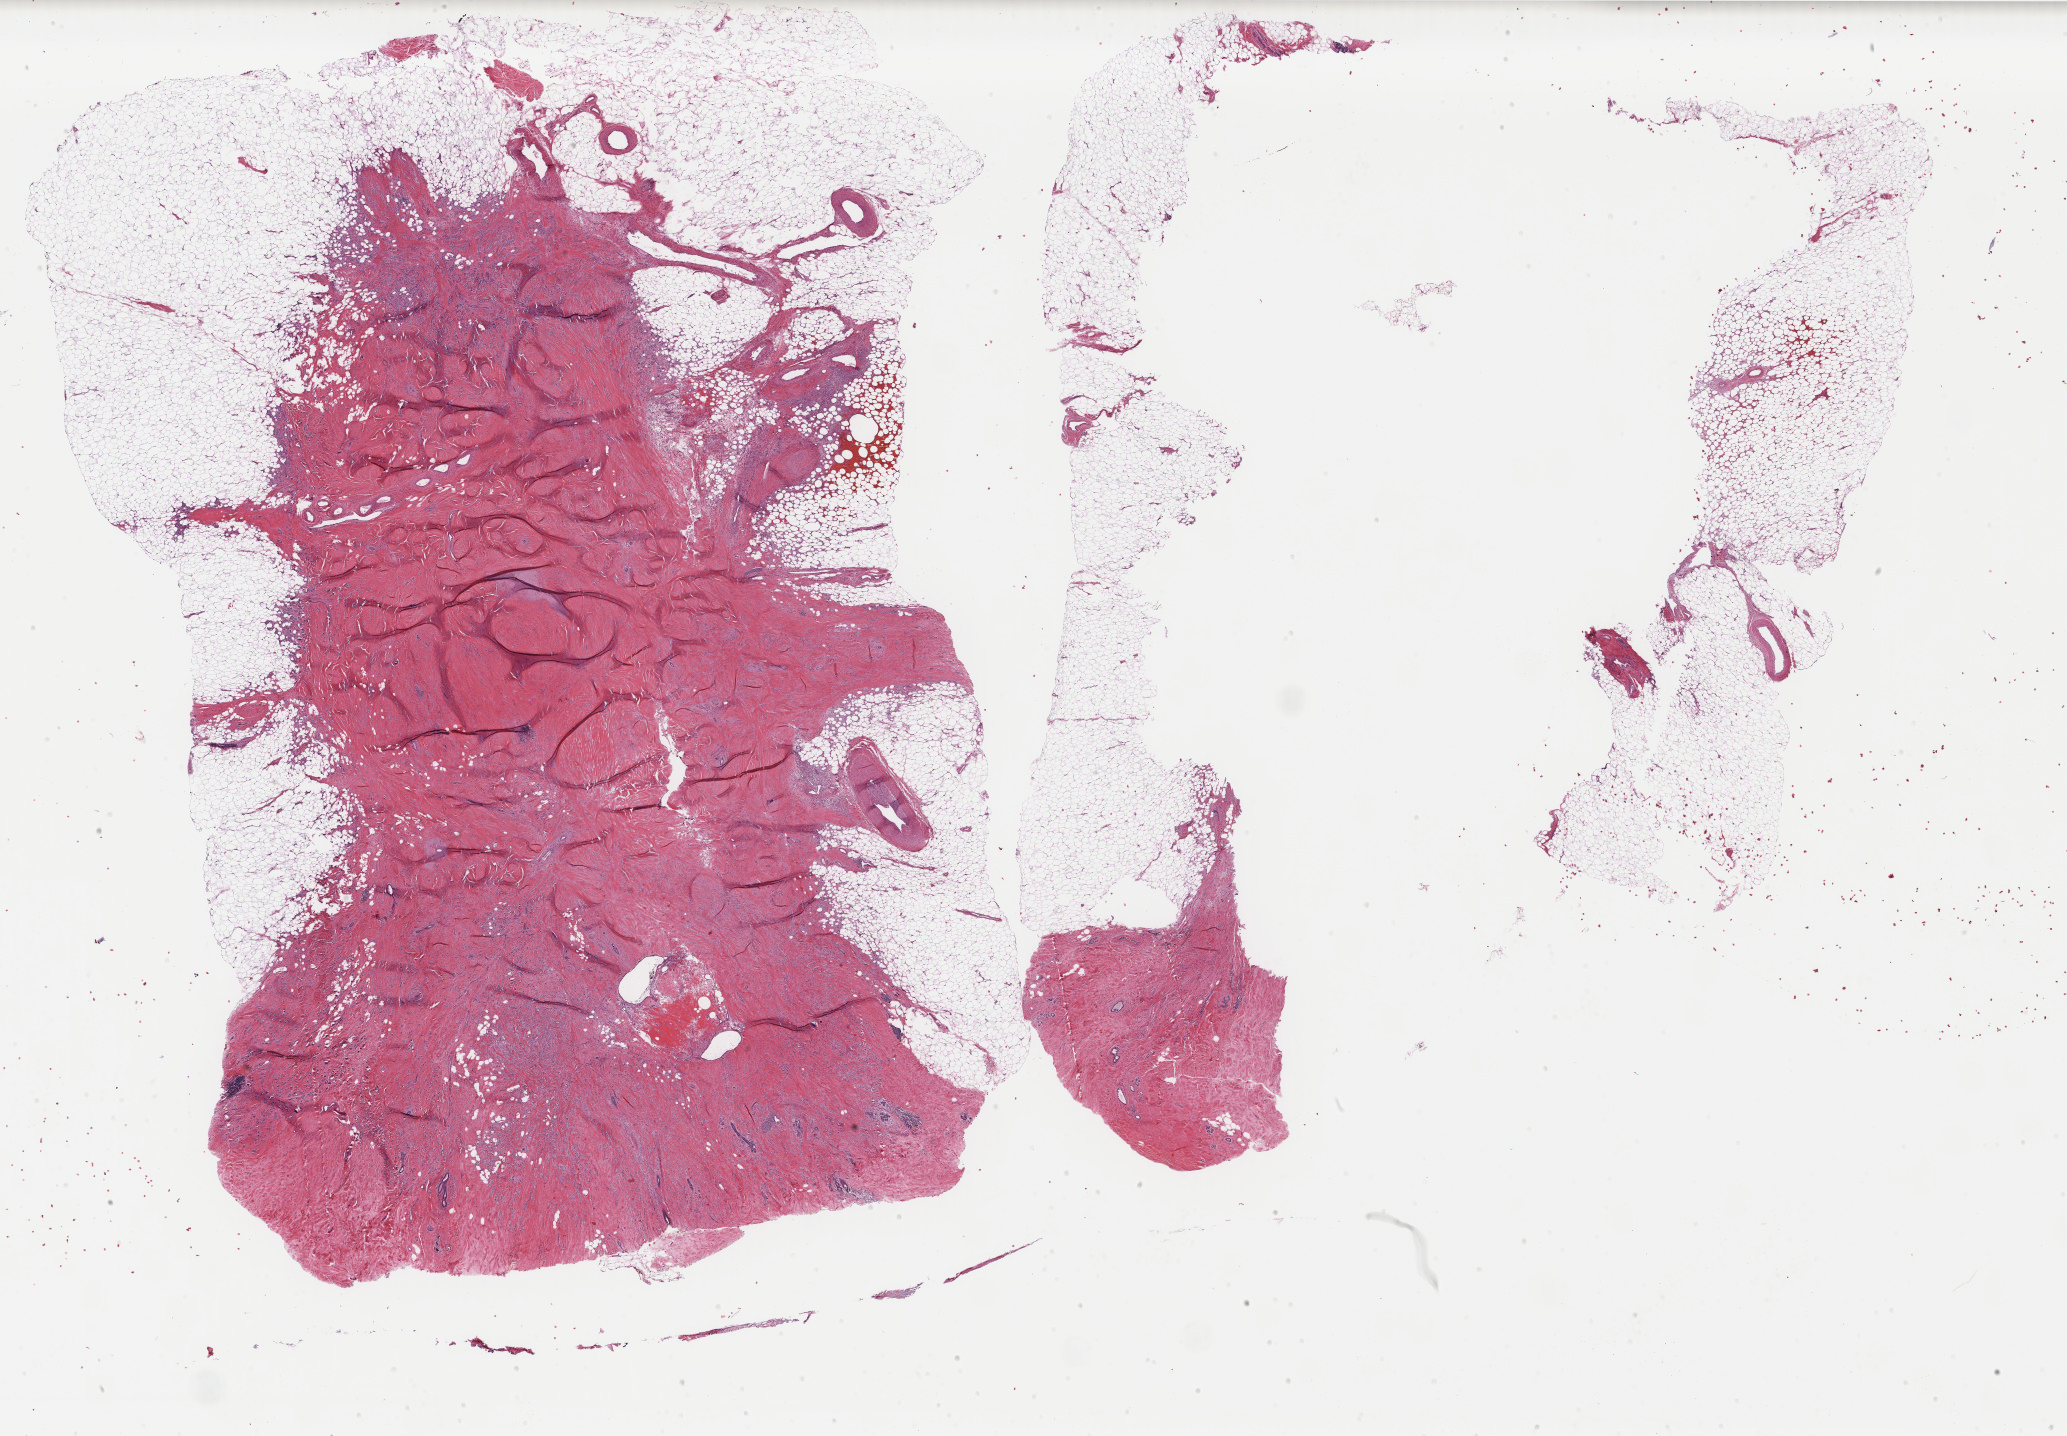
Whole-slide histology image, H&E — whole scanned area (about 32.8 x 22.8 mm, from a 40x scan) shown as a low-resolution overview. FFPE section. Sample: primary tumour, breast. Female patient; age at initial diagnosis 65 years.
• pathologic diagnosis: Lobular carcinoma, NOS
• lymph nodes positive (case pathology): 0 of 2 examined
• laterality: right
• AJCC pathologic stage: IIA (7th edition)